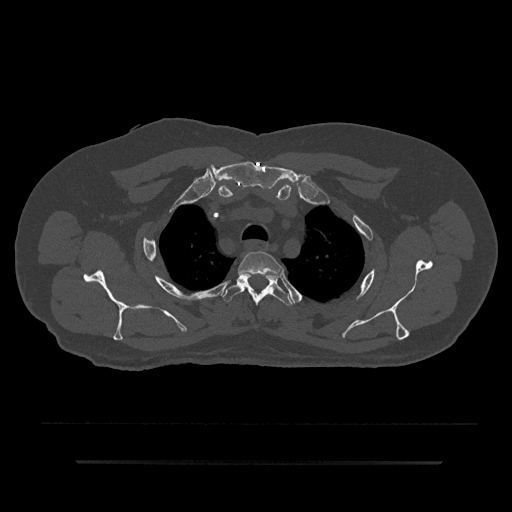
CT including the spine, one axial slice; position 673 of 797 along the scan axis; reconstruction kernel Br40s/3; bone window (W 1800 / L 400 HU); 0.5 mm slice thickness; 512 × 512 image matrix. Male patient, age 59 years. From the clinical record (not read from this slice): primary cancer: bile ducts.
Outlined on this slice (semi-automatically segmented with operator editing):
- T2 vertebra: bounding box <238,251,282,276> (left, top, right, bottom; pixels)
- T3 vertebra: <223,273,293,306>